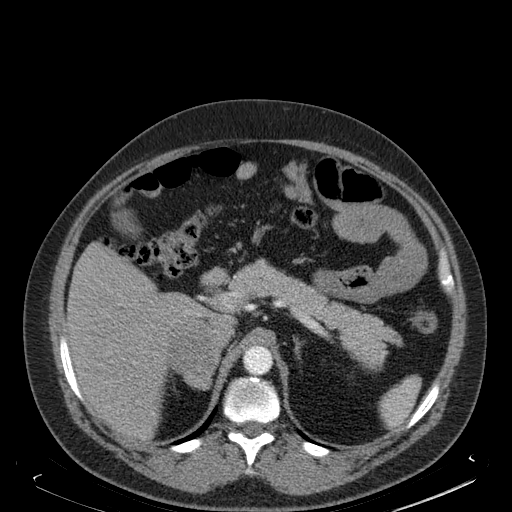
Contrast-enhanced abdominal CT, one axial slice; slice 119 of 181 in the series (ordered by position); soft-tissue window (W 400 / L 40 HU); 1.5 mm slice thickness; 512 × 512 image matrix, field of view 405 × 405 mm. Male patient. From the clinical record (not read from this slice): diagnosis: adrenocortical carcinoma; tumour side: right adrenal; tumour size at pathology: 7.5 cm.
Structures marked on this image (semi-automatic segmentation, software-assisted and operator-edited):
- mass: box from (x=168, y=317) to (x=219, y=387) px